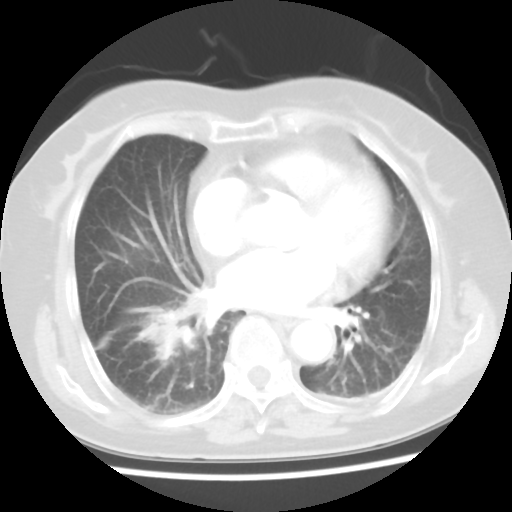
Chest CT, one axial slice; slice 19 of 45 in the series (ordered by position); 120 kVp; lung window (W 1500 / L -600 HU); 5 mm slice thickness; 512 × 512 image matrix, field of view 312 × 312 mm. Female patient, age 65 years. From the clinical record (not read from this slice): clinical TNM (as recorded): T2 N3 M0.
Annotated regions visible in this slice (rectangle marked by the reading radiologist):
- lung tumour (recorded histology: adenocarcinoma): bounding box (x1, y1, x2, y2) in pixels: (131, 303, 201, 370)